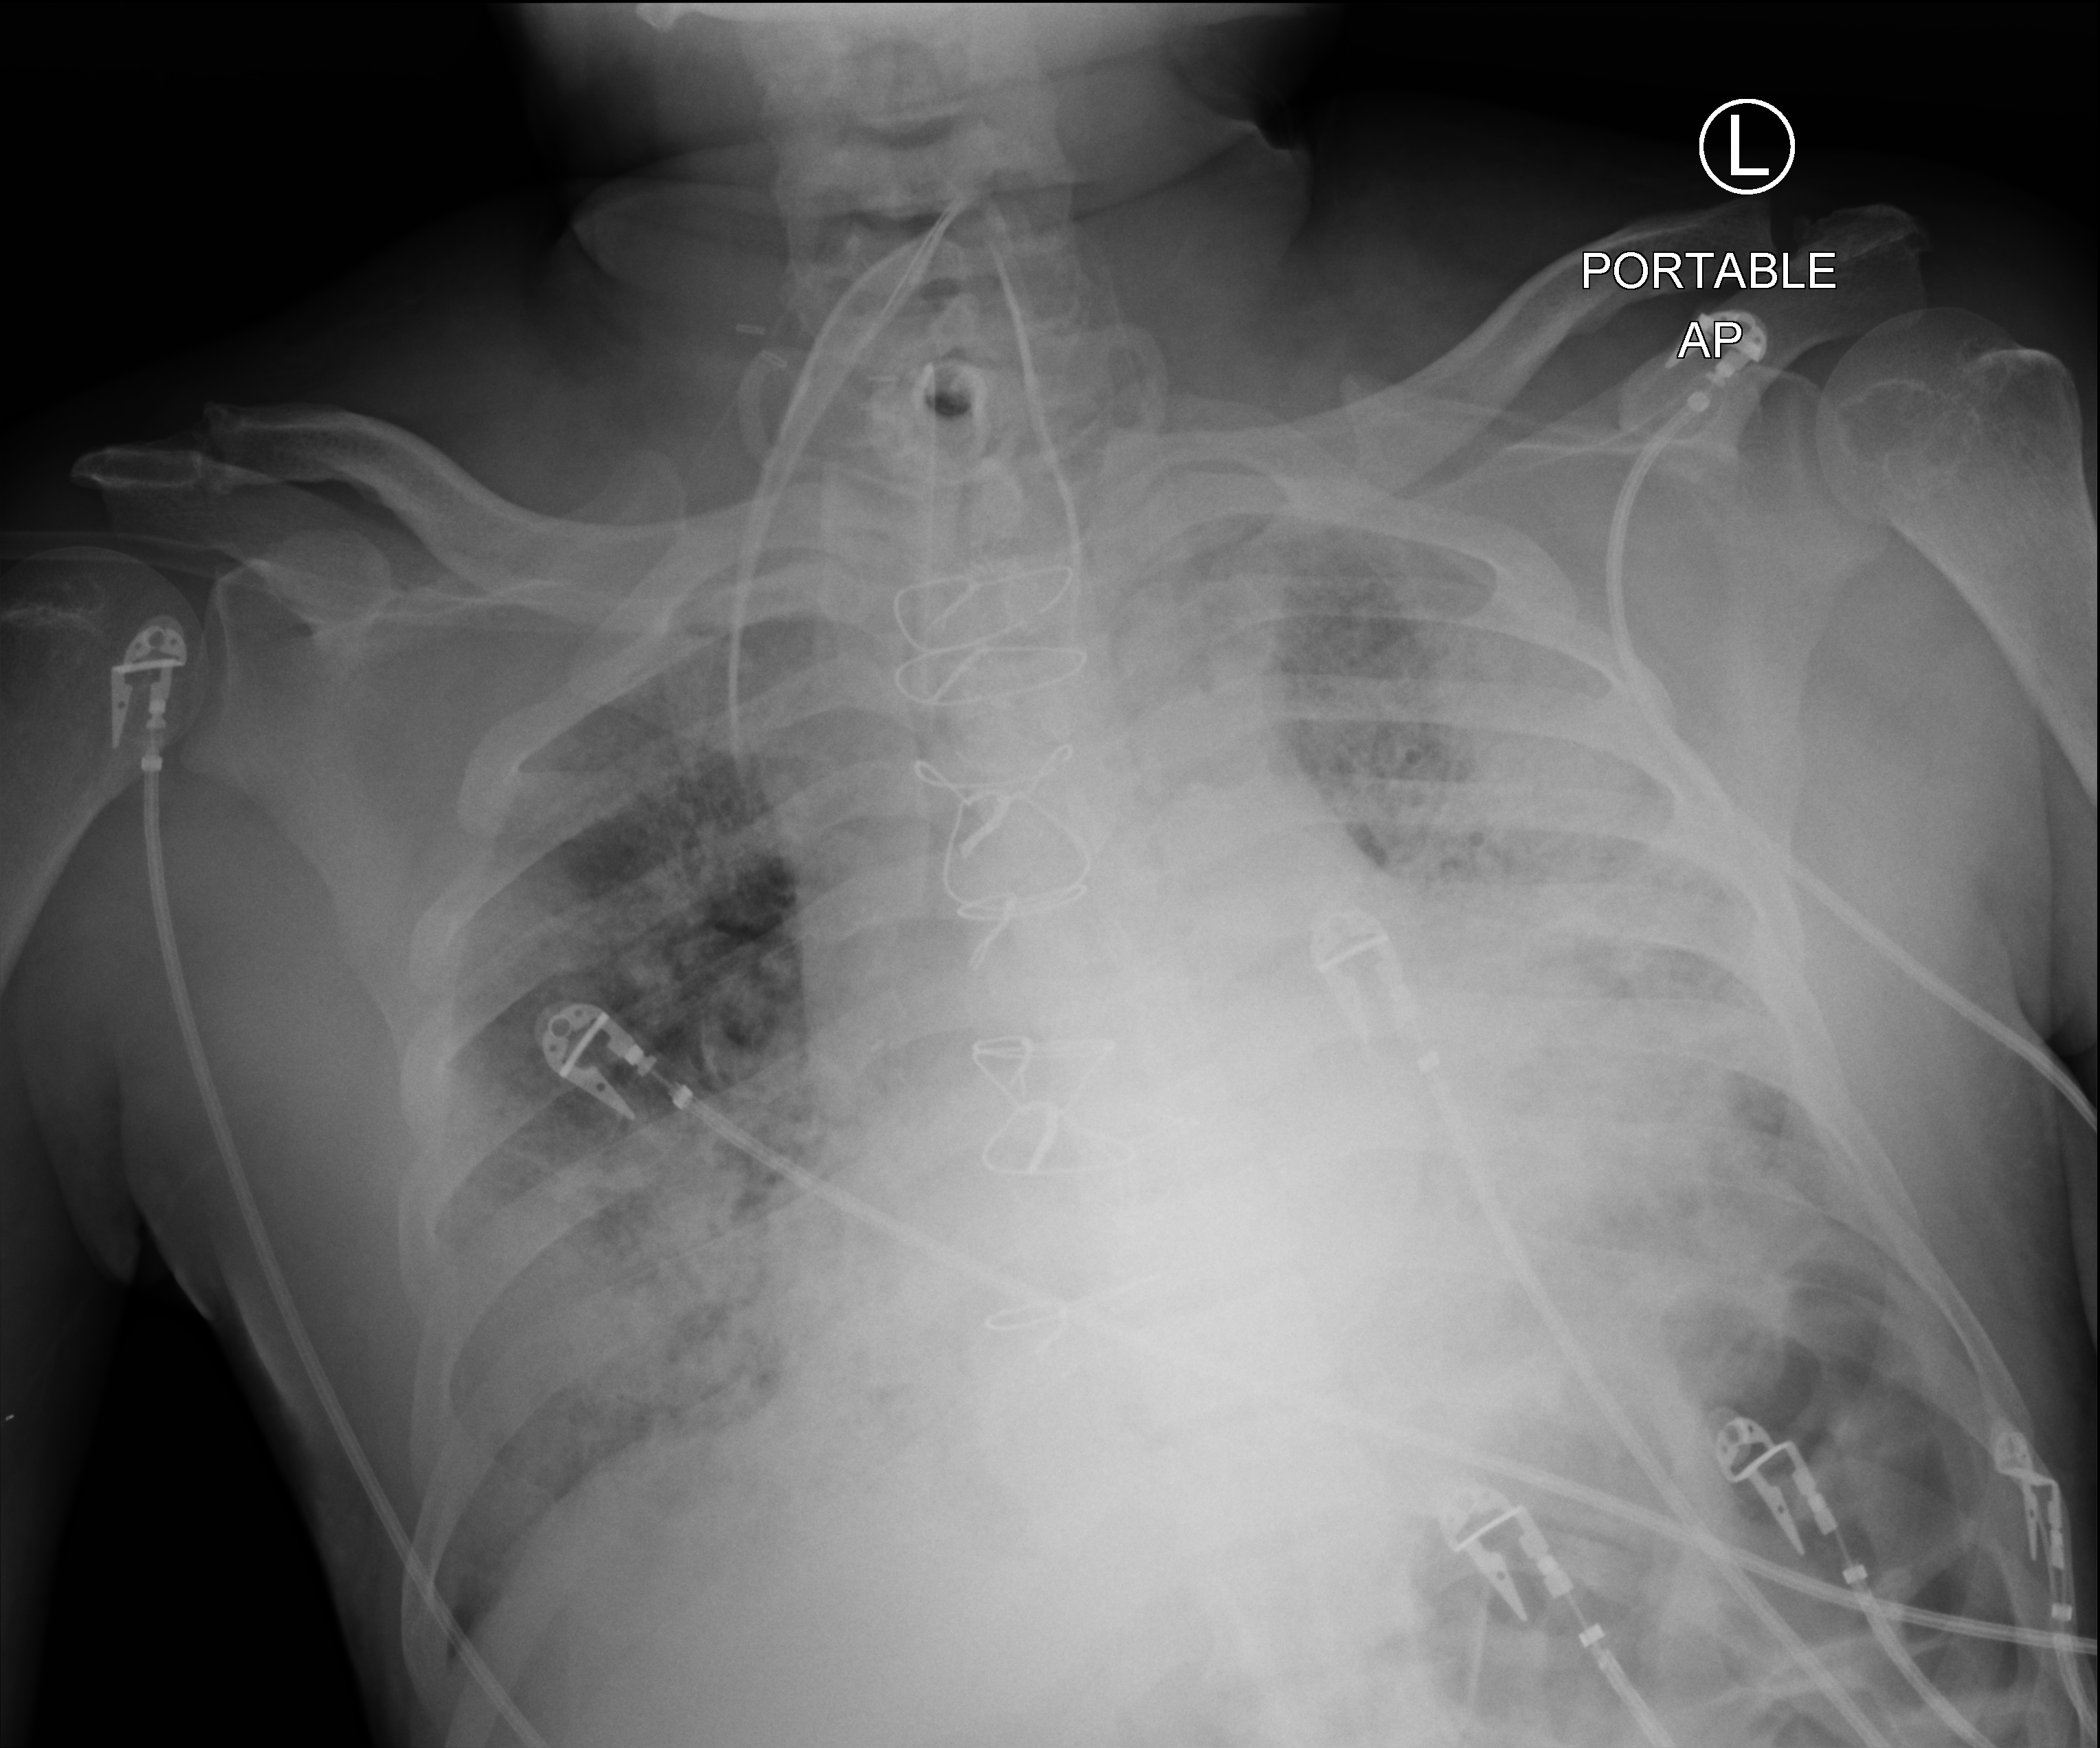
Portable chest radiograph. Male patient hospitalised with COVID-19, age 60–74 years.
From the hospital-stay record, not from the radiograph (when in the stay this image was taken is not recorded): admitted to intensive care during this hospital stay: yes; length of hospital stay: 50 days; mechanically ventilated during this hospital stay: yes.